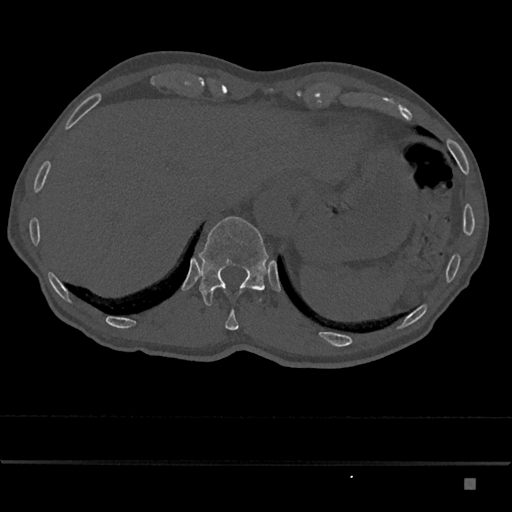
CT including the spine, one axial slice. Slice 635 of 797 in the series (ordered by position). Reconstruction kernel Br40s/3. 120 kVp. Bone window (W 1800 / L 400 HU). 0.5 mm slice thickness. 512 × 512 image matrix. Patient: male, 72 years. Case-level facts recorded for this patient, not image findings: primary cancer: prostate.
Outlined on this slice (semi-automatic segmentation, software-assisted and operator-edited):
- T11 vertebra: bounding box (x1, y1, x2, y2) in pixels: (225, 309, 239, 330)
- T12 vertebra: (199, 216, 269, 306)